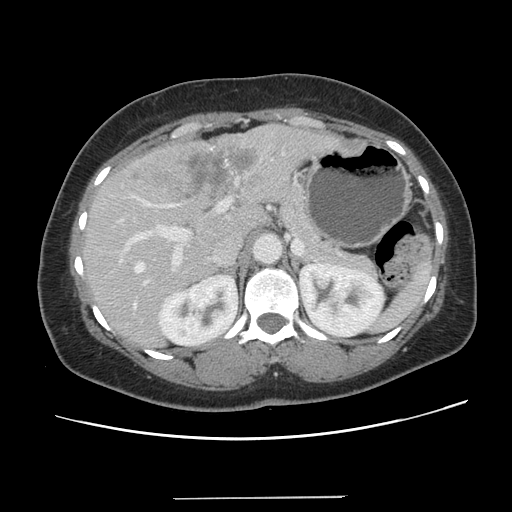
Contrast-enhanced abdominal CT, one axial slice. Position 83 of 141 along the scan axis. 120 kVp. Intravenous contrast given. Soft-tissue window (W 400 / L 40 HU). 512 × 512 image matrix, field of view 366 × 366 mm. Female patient, age 53 years. From the clinical record (not read from this slice): diagnosis: colorectal cancer liver metastases, imaged before liver resection; multiple liver metastases: no; largest metastasis: 14.5 cm; disease in both lobes: yes.
Annotated regions visible in this slice (manually delineated by an expert):
- hepatic veins: box from (x=134, y=202) to (x=173, y=307) px
- liver: (x=83, y=126)–(x=339, y=346)
- planned liver remnant (the part of the liver to remain after resection): (x=84, y=206)–(x=263, y=347)
- portal vein (with intrahepatic branches): (x=129, y=200)–(x=228, y=286)
- liver metastasis: (x=134, y=144)–(x=261, y=202)